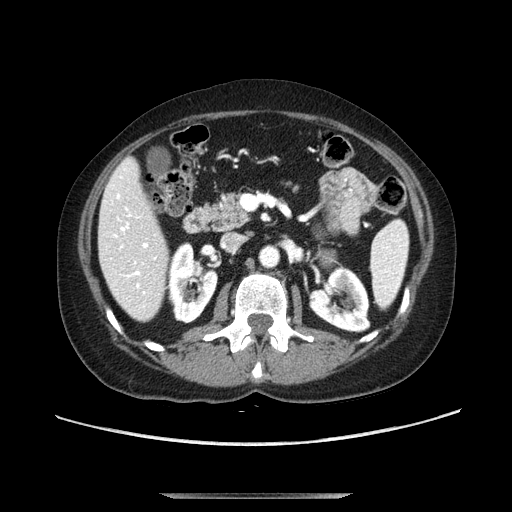
Contrast-enhanced abdominal CT, one axial slice. Position 52 of 107 along the scan axis. Soft-tissue window (W 400 / L 40 HU). 512 × 512 image matrix, field of view 380 × 380 mm. Female patient. From the clinical record (not read from this slice): diagnosis: adrenocortical carcinoma; tumour side: left adrenal; tumour size at pathology: 7.5 cm; Ki-67 index: 9 %; stage (as recorded): 3.
Structures marked on this image (semi-automatic segmentation, software-assisted and operator-edited):
- mass: bounding box [x1, y1, x2, y2] px = [320, 248, 337, 268]